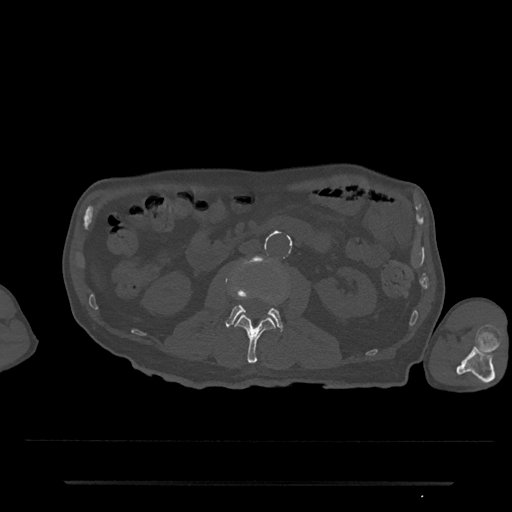
CT including the spine, one axial slice. 120 kVp. Bone window (W 1800 / L 400 HU). 512 × 512 image matrix, field of view 427 × 427 mm. Male patient, age 74 years. Case-level facts recorded for this patient, not image findings: primary cancer: prostate.
Annotated regions visible in this slice (semi-automatically segmented with operator editing):
- L2 vertebra: bounding box <236,315,275,364> (left, top, right, bottom; pixels)
- L3 vertebra: <225,256,284,332>